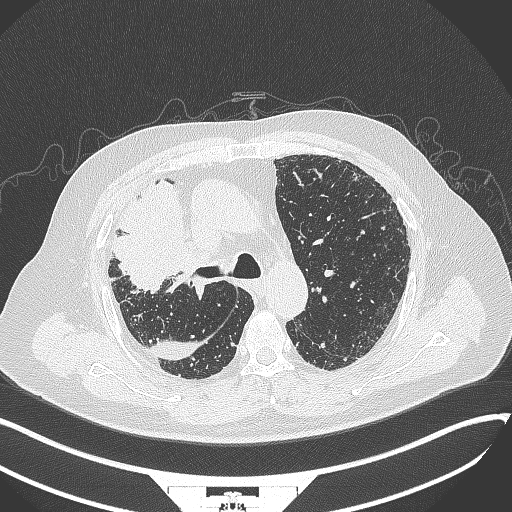
Chest CT, one axial slice. Slice 244 of 384 in the series (ordered by position). Reconstruction kernel B70f. 120 kVp. Lung window (W 1500 / L -600 HU). 1 mm slice thickness. 512 × 512 image matrix. Patient: male, 69 years. From the clinical record (not read from this slice): clinical TNM (as recorded): T4 N3 M1.
Structures marked on this image (rectangle marked by the reading radiologist):
- lung tumour (recorded histology: adenocarcinoma): bounding box (x1, y1, x2, y2) in pixels: (102, 173, 187, 300)